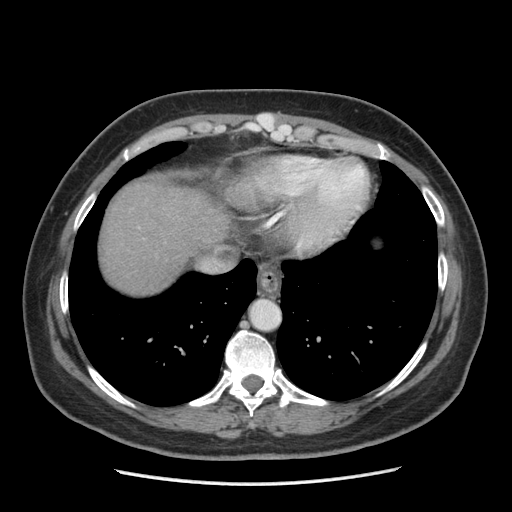
Contrast-enhanced abdominal CT (liver protocol), one axial slice. Position 172 of 185 along the scan axis. Reconstruction kernel STANDARD. Soft-tissue window (W 400 / L 40 HU). 2.5 mm slice thickness. 512 × 512 image matrix. From the clinical record (not read from this slice): diagnosis: hepatocellular carcinoma (patient treated with transarterial chemoembolisation; whether this scan precedes or follows treatment is not stated here); TNM stage (as recorded): Stage-I; Child-Pugh class: A; tumour nodularity: uninodular.
Structures marked on this image (semi-automatically segmented with operator editing):
- liver parenchyma outside the tumour (the mass and vessels are separate outlines, so this box may not span the whole liver): bounding box [x1, y1, x2, y2] px = [100, 180, 232, 294]